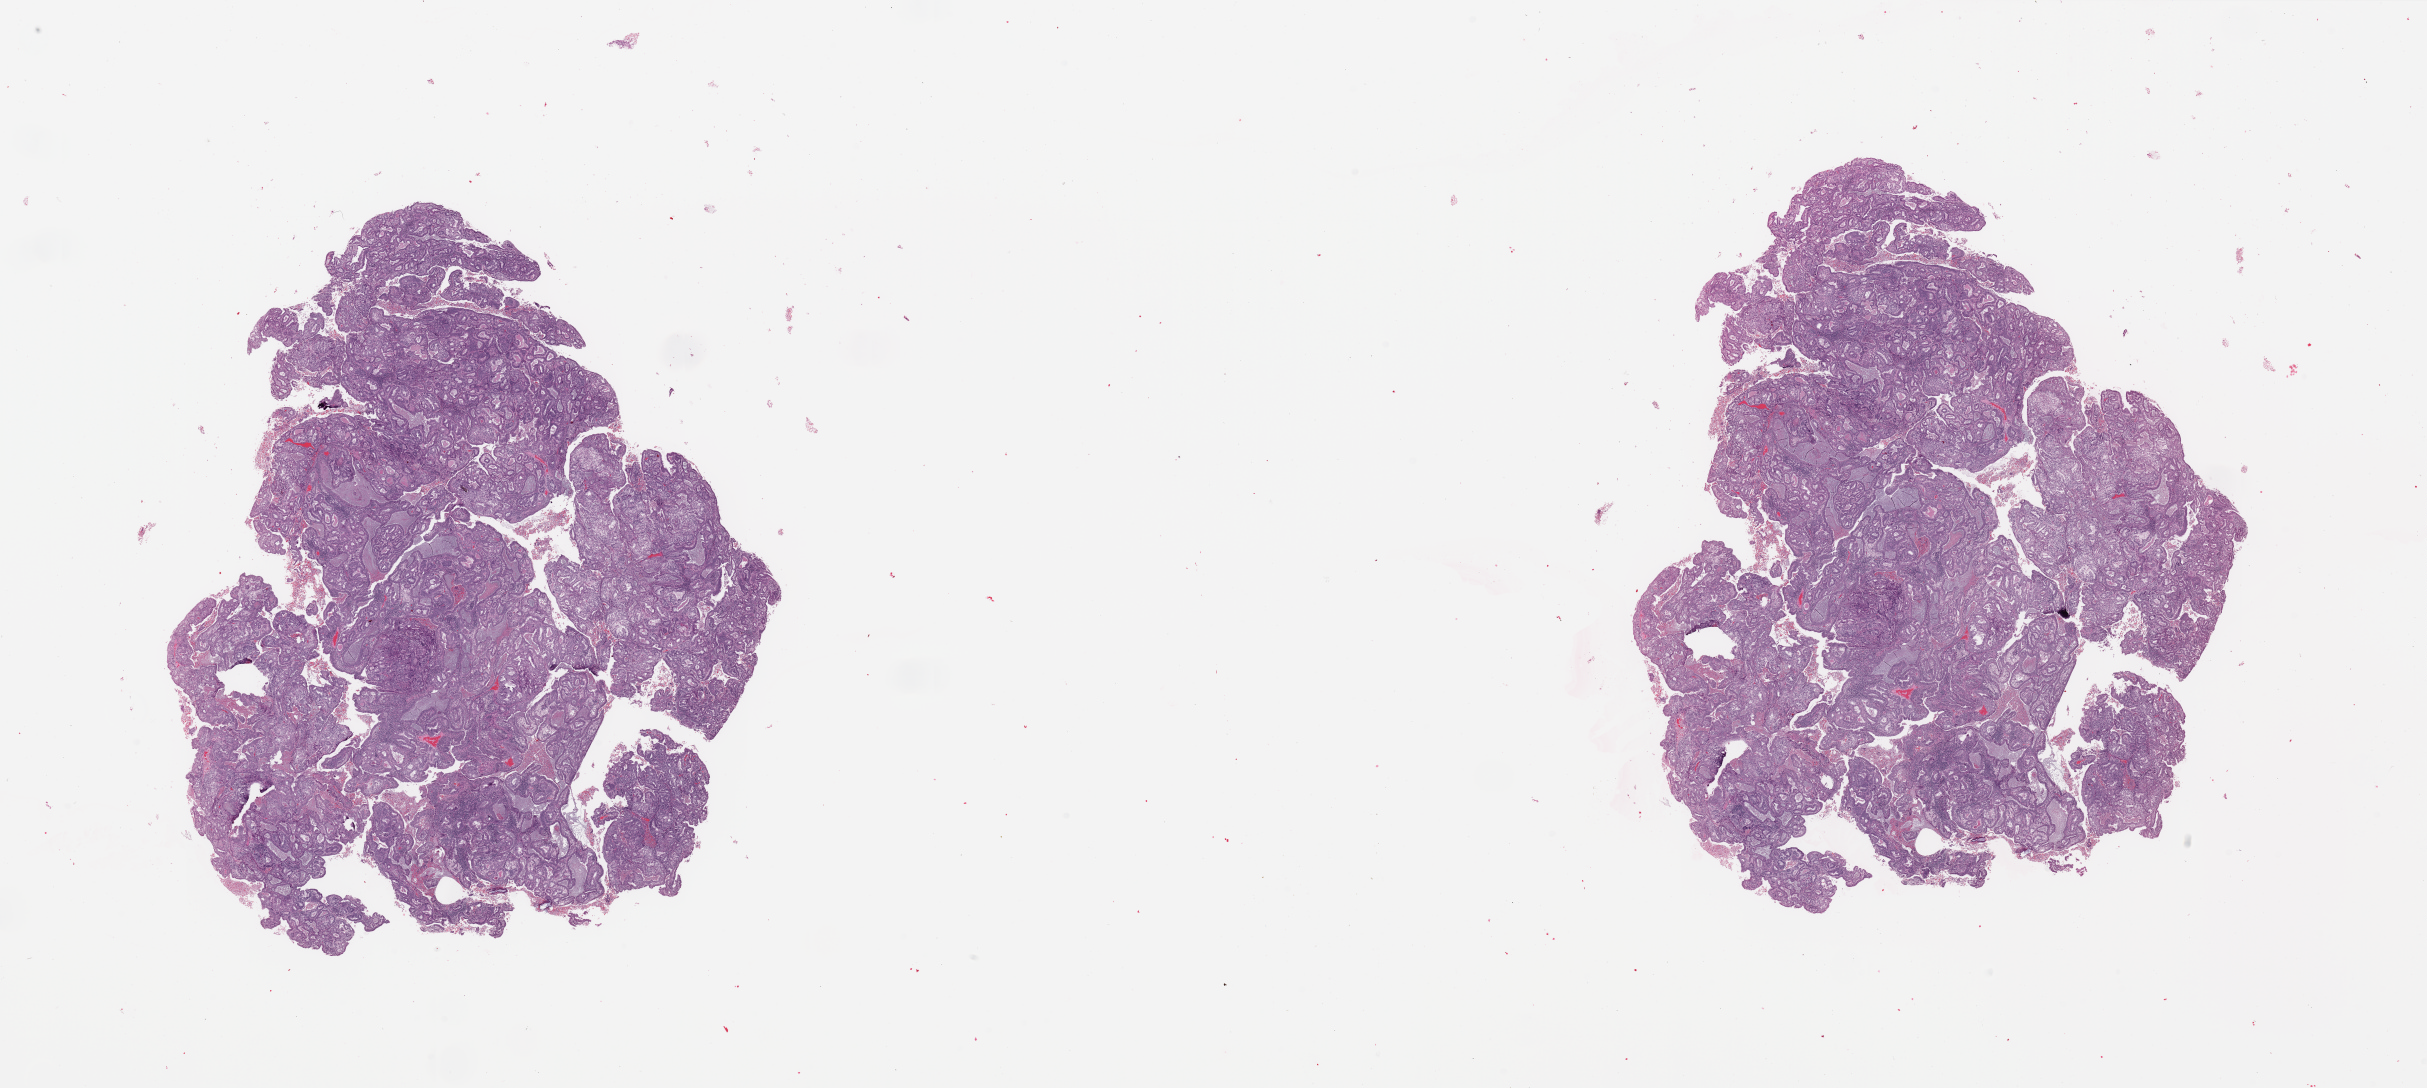
H&E-stained whole-slide image, a low-resolution overview of the entire scanned area, about 38.4 x 17.2 mm (slide scanned at 20x); tumour tissue sample, sampled site: uterus. Female, 72 y/o. Histologic grade: G2 (moderately differentiated). Slide review estimates, as recorded: tumour nuclei 95%, necrosis 1%.
Diagnosis: Endometrioid adenocarcinoma, NOS. AJCC pathologic stage: I.